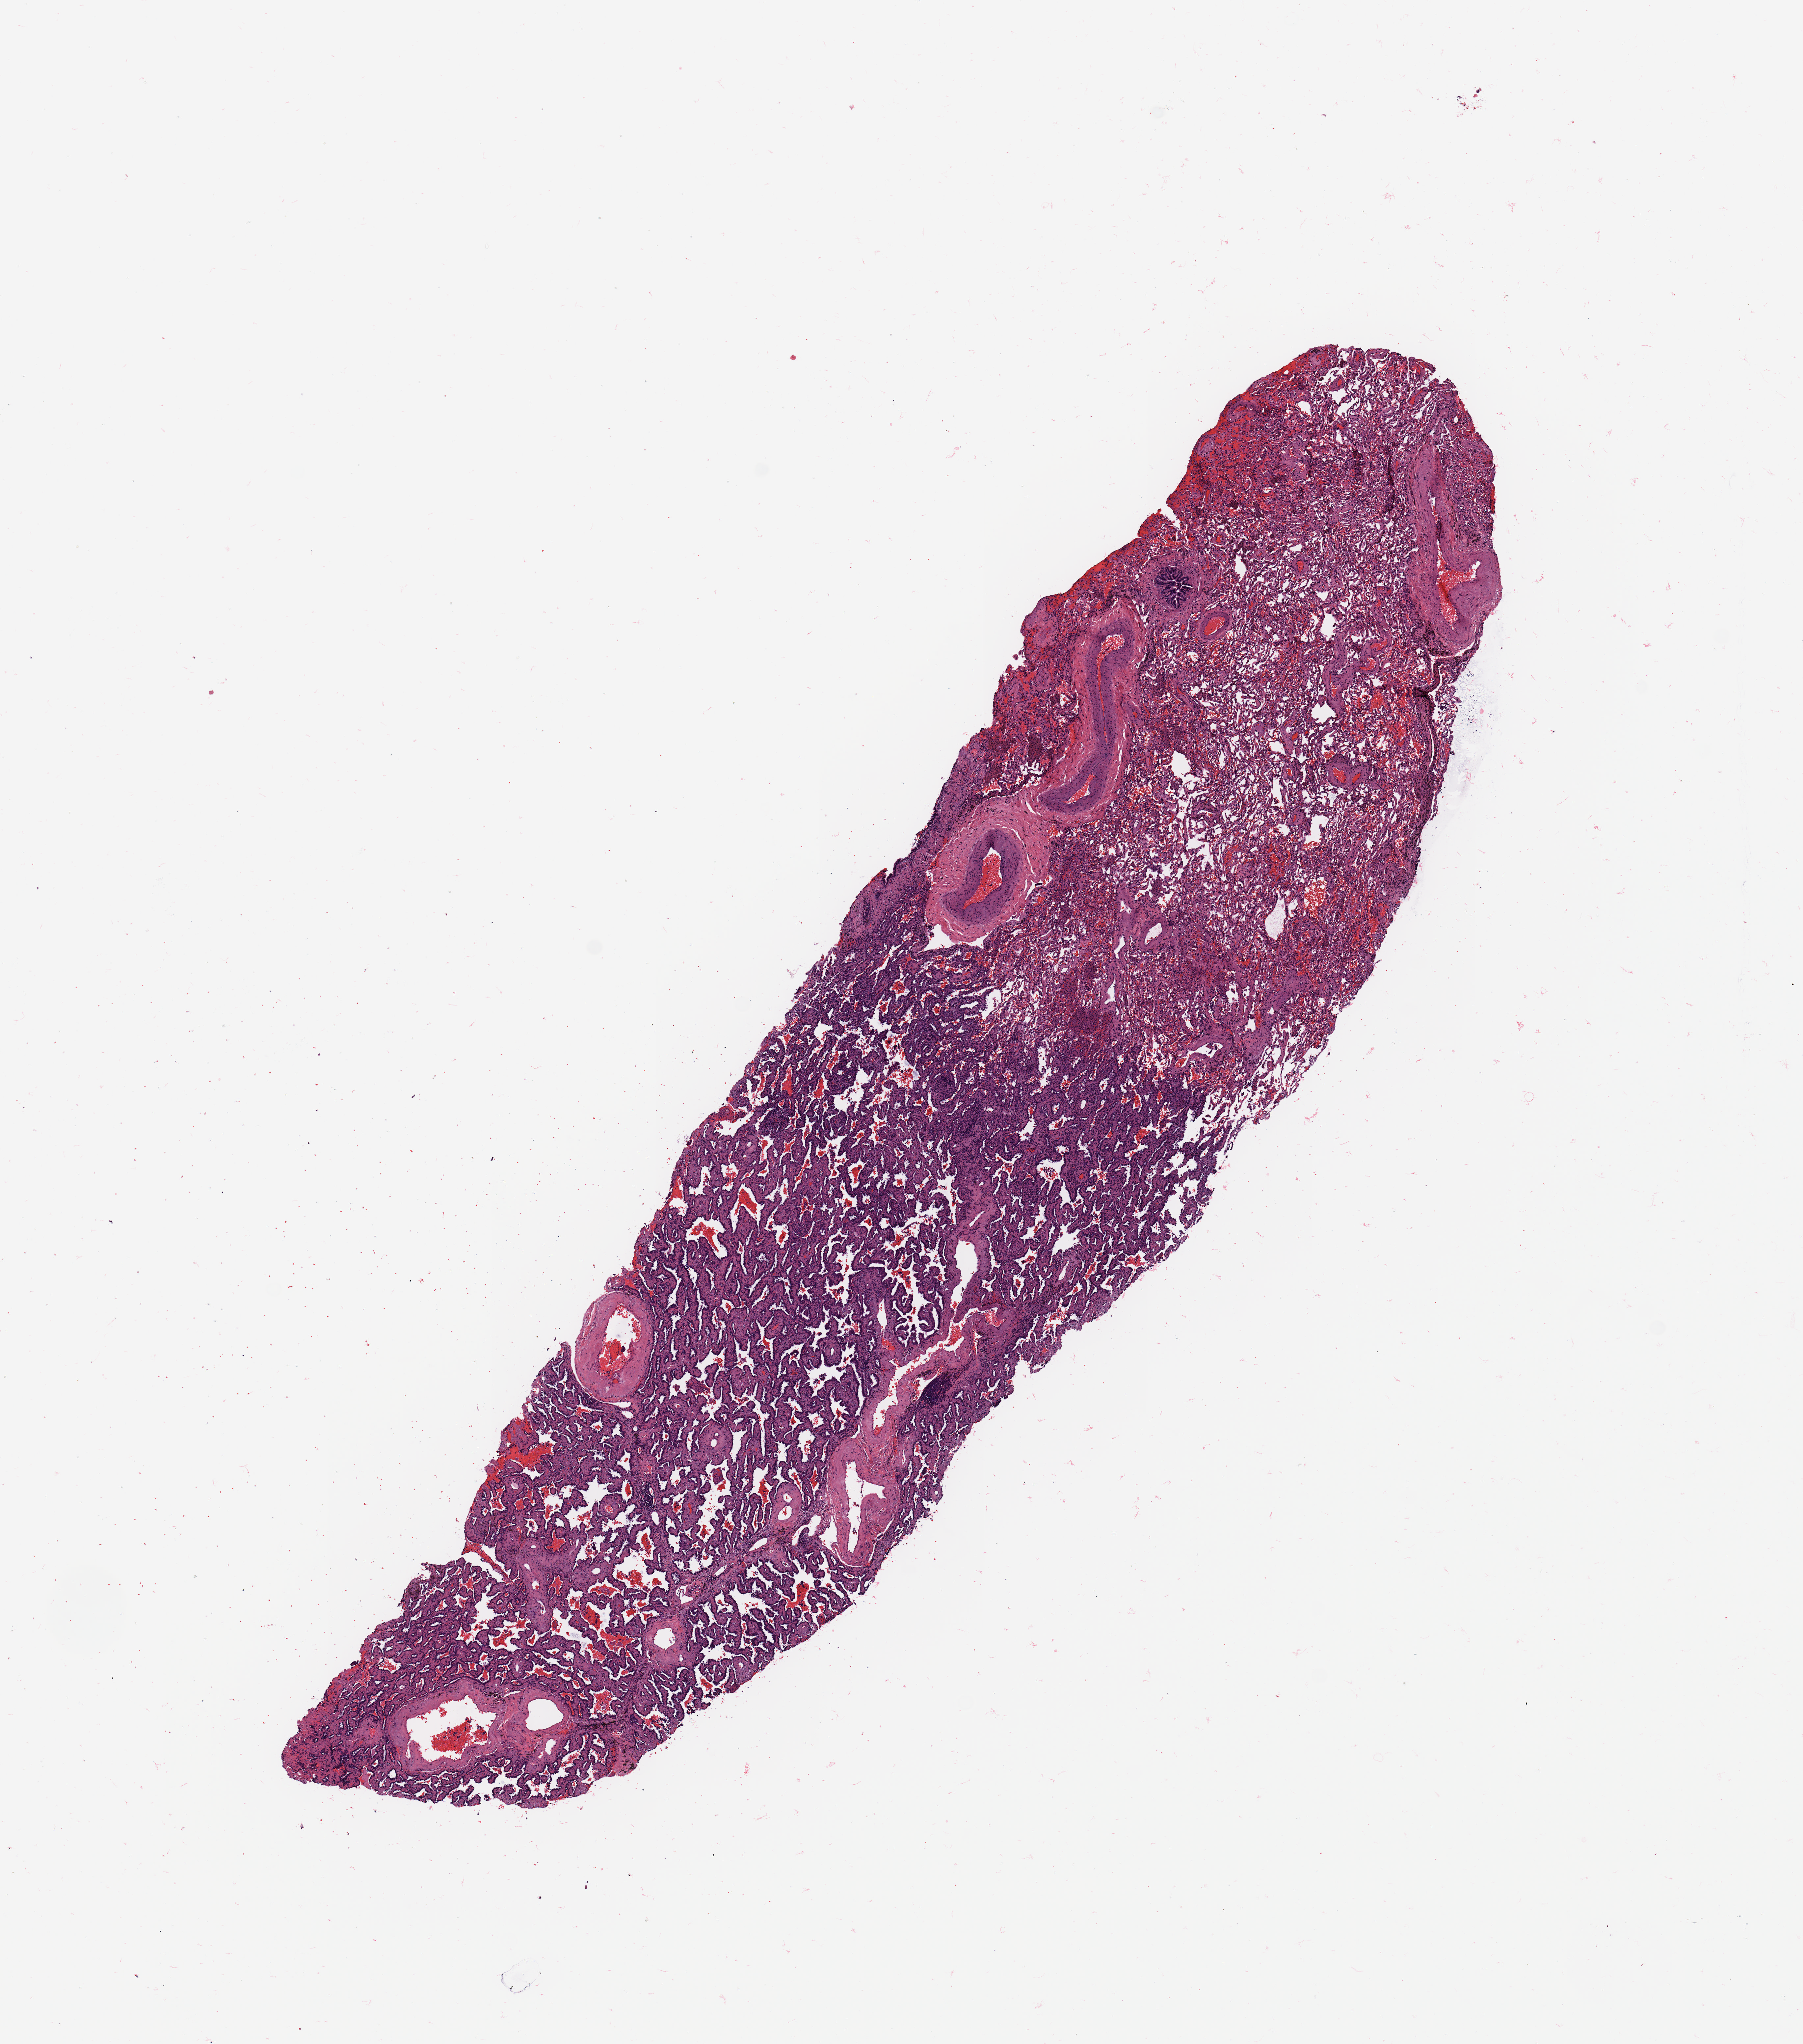
H&E-stained whole-slide image — a low-resolution overview of the entire scanned area, about 10.8 x 12.3 mm (slide scanned at 20x); lung, tumour tissue. Patient: male, age 71 years. Histologic grade: G1 (well differentiated).
• diagnosis: Adenocarcinoma, NOS
• AJCC pathologic stage: IB
• primary tumour site (as recorded): right lower lobe